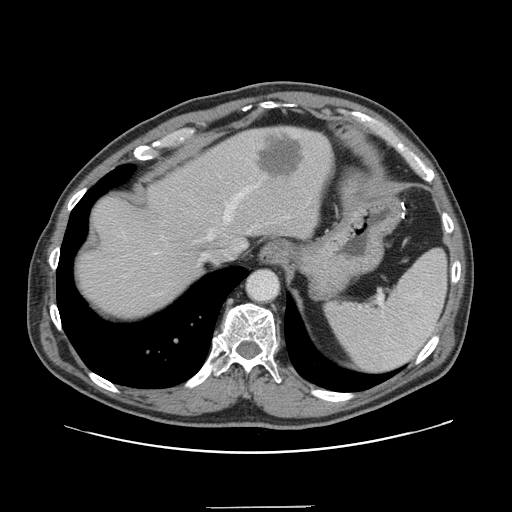
Contrast-enhanced abdominal CT, one axial slice; slice 120 of 139 in the series (ordered by position); intravenous contrast given; soft-tissue window (W 400 / L 40 HU); 2.5 mm slice thickness; 512 × 512 image matrix, field of view 397 × 397 mm. Male patient, age 64 years. From the clinical record (not read from this slice): diagnosis: colorectal cancer liver metastases, imaged before liver resection; multiple liver metastases: yes; largest metastasis: 3.5 cm; chemotherapy before resection: yes.
Annotated regions visible in this slice (outlined manually by an expert reader):
- hepatic veins: box from (x=224, y=189) to (x=247, y=221) px
- liver: (x=77, y=127)–(x=331, y=319)
- planned liver remnant (the part of the liver to remain after resection): (x=77, y=132)–(x=263, y=320)
- liver metastasis: (x=258, y=136)–(x=303, y=179)